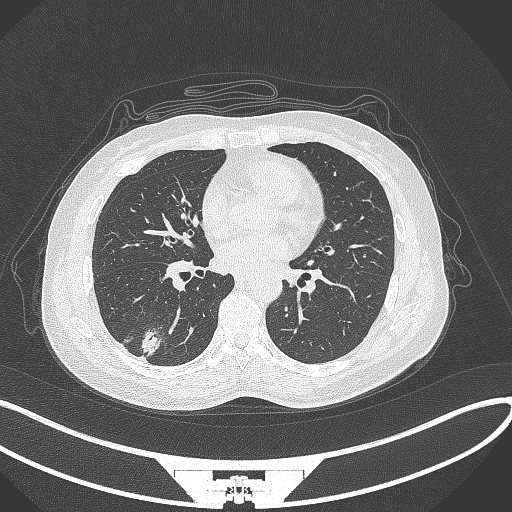
Chest CT, one axial slice. Slice 135 of 352 in the series (ordered by position). 120 kVp. Lung window (W 1500 / L -600 HU). 1 mm slice thickness. 512 × 512 image matrix, field of view 400 × 400 mm. Patient: female, 55 years. Case-level facts recorded for this patient, not image findings: clinical TNM (as recorded): T1c N1 M0.
Outlined on this slice (rectangle marked by the reading radiologist):
- lung tumour (recorded histology: adenocarcinoma): bounding box (x1, y1, x2, y2) in pixels: (139, 325, 169, 361)